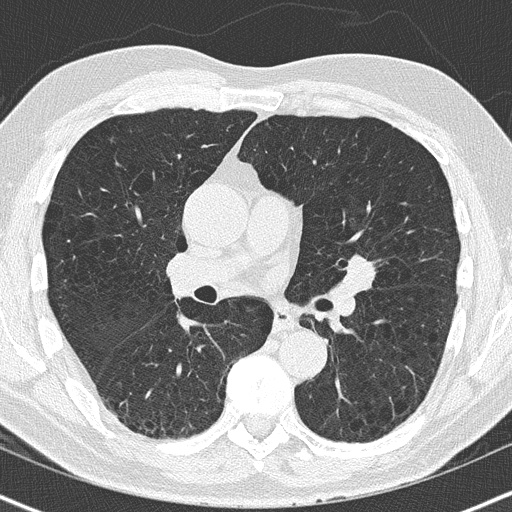
Chest CT (low-dose screening protocol), one axial image; first (baseline) screen; lung window (W 1500 / L -600 HU); 2 mm slice thickness; 512 × 512 image matrix, field of view 320 × 320 mm. Male participant, aged 63 years at enrolment.
Lesion marked by an expert reader, bounding box (x1, y1, x2, y2) in pixels: (334, 254, 381, 292). The screening reader recorded 2 non-calcified nodules or masses ≥4 mm on this exam (lingula, right lower lobe); which of them this box marks is not recorded. Lung cancer was diagnosed 32 days after this screen: squamous cell carcinoma, NOS, left upper lobe, moderately differentiated (G2), stage IA (AJCC 6th edition), 23 mm at pathology.